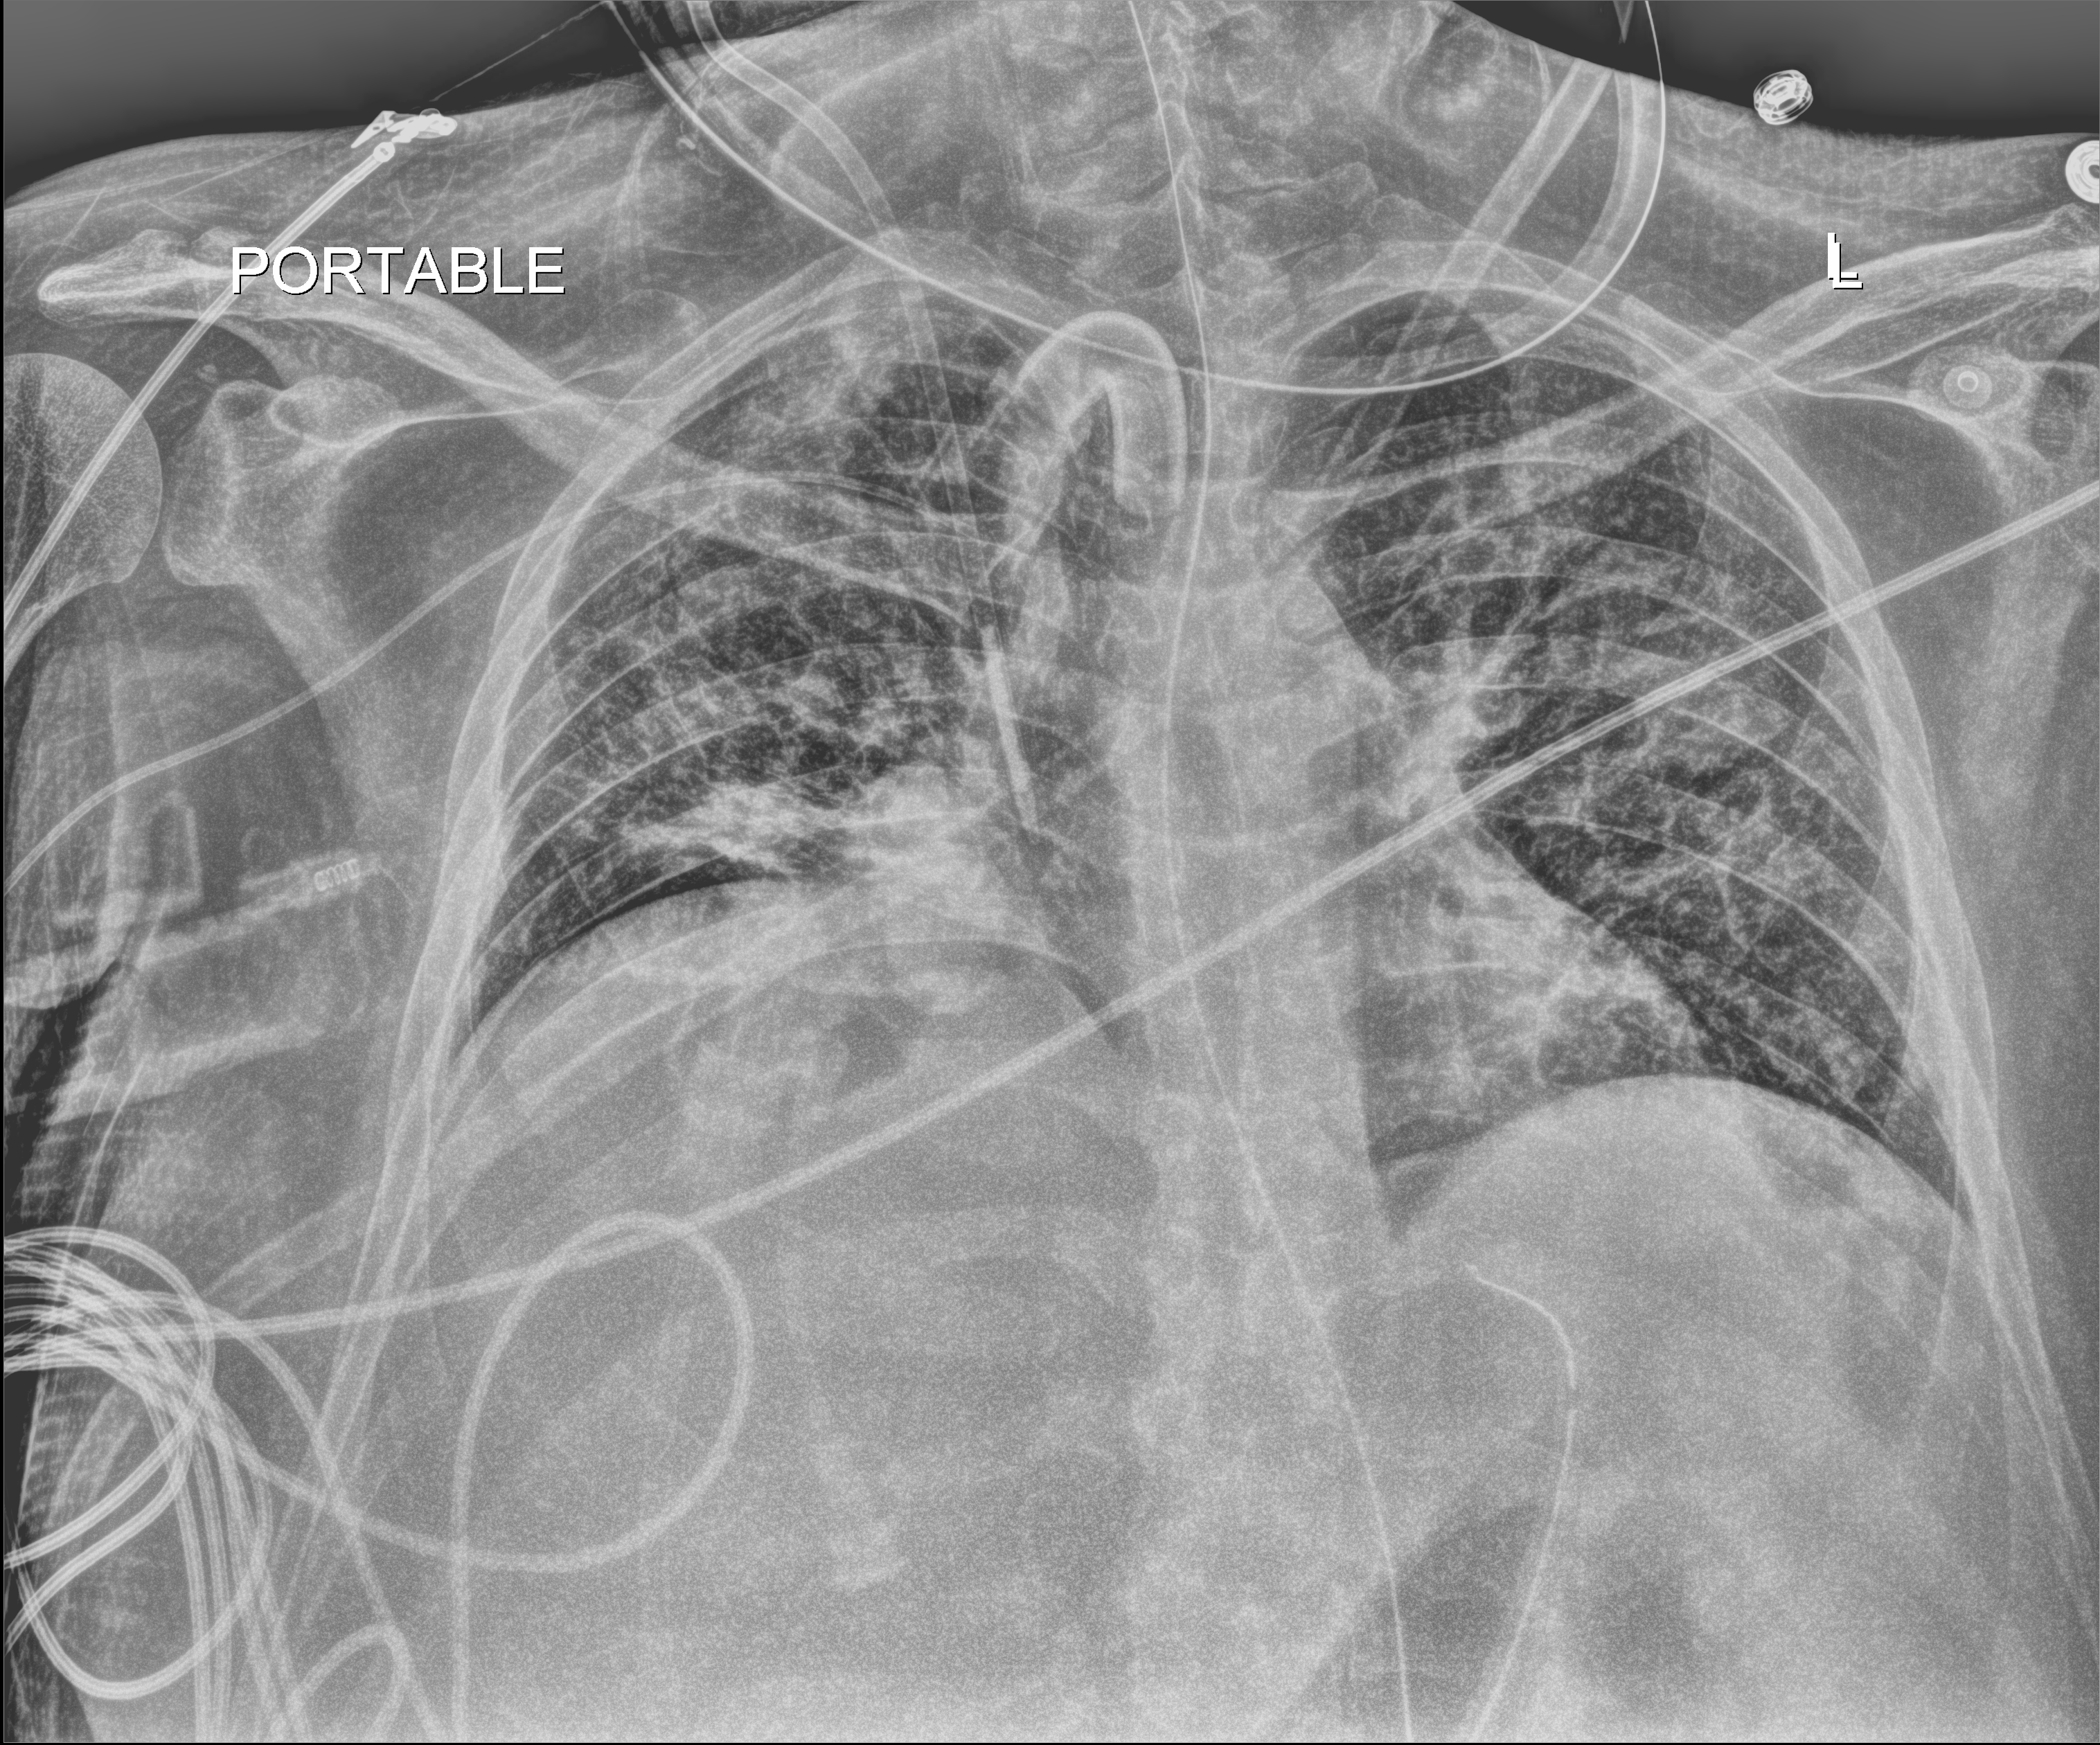
Chest X-ray (portable); anteroposterior (AP) projection. Patient hospitalised with COVID-19, aged 18–59 years.
From the hospital-stay record, not from the radiograph (when in the stay this image was taken is not recorded):
- length of hospital stay: 50 days
- admitted to intensive care during this hospital stay: yes
- mechanically ventilated during this hospital stay: yes